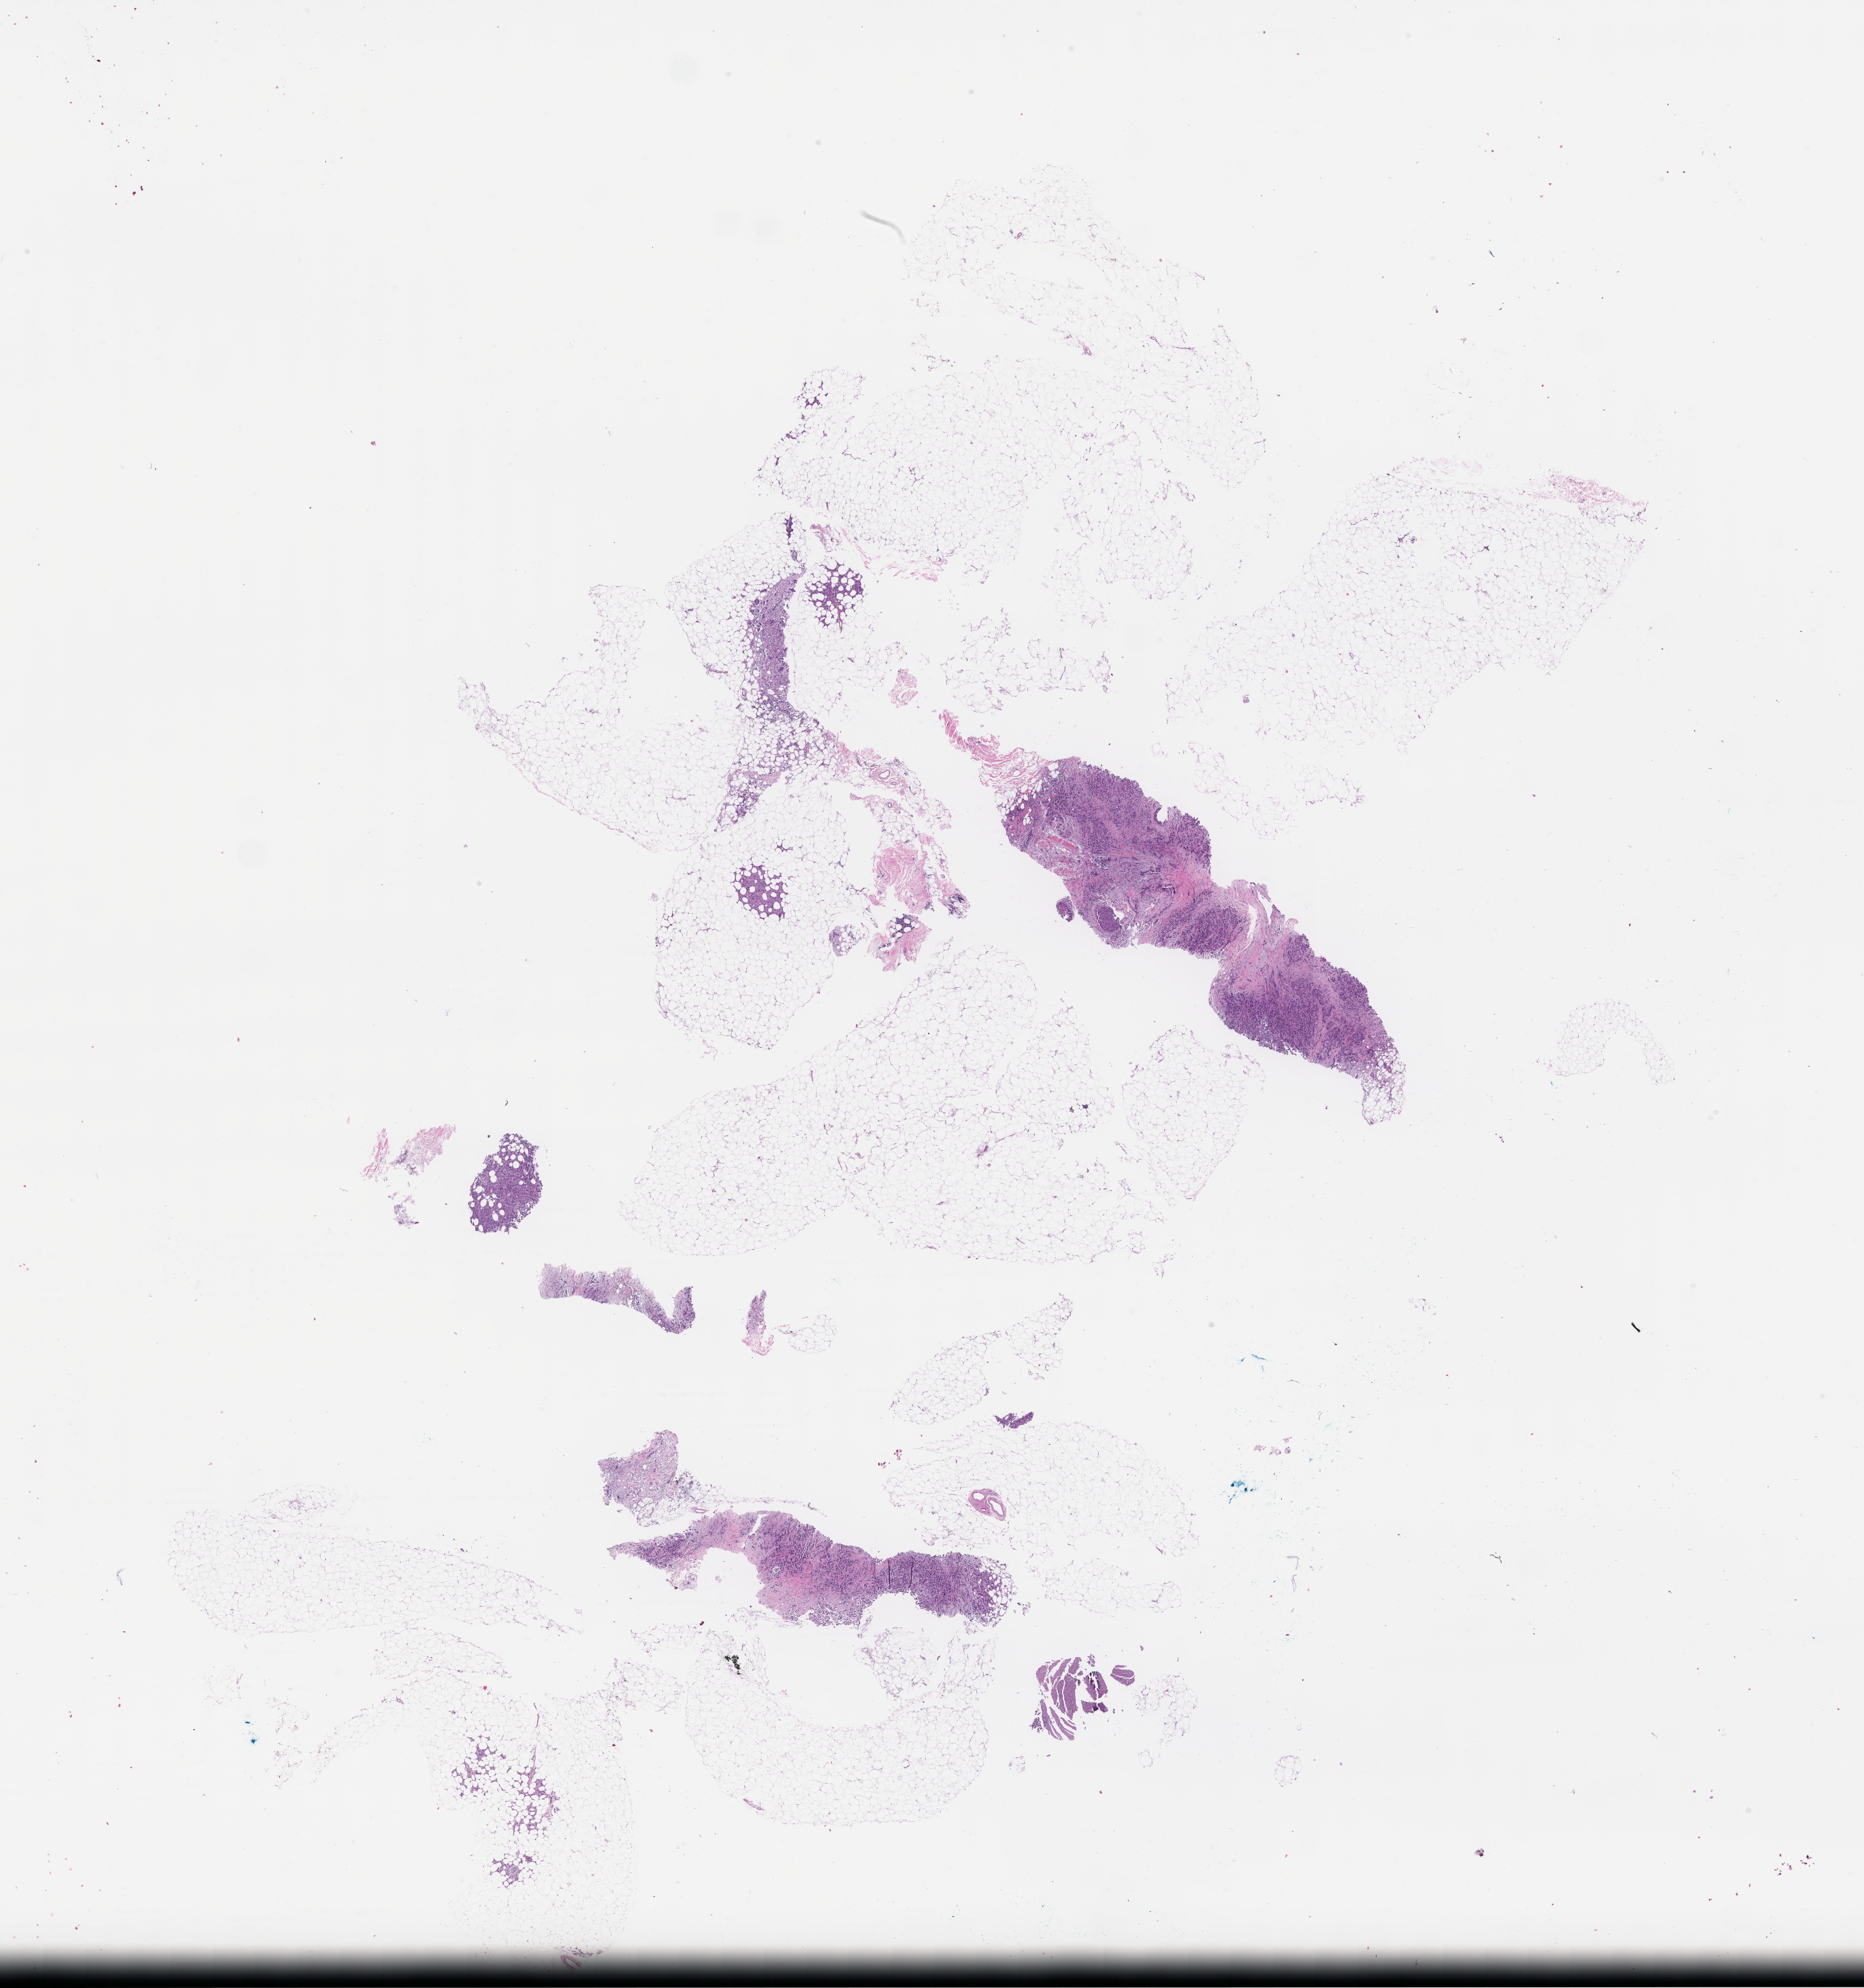
Whole-slide image, hematoxylin and eosin (H&E) stain, whole scanned area (about 22.1 x 23.6 mm) shown as a low-resolution overview, formalin-fixed, paraffin-embedded (FFPE) tissue, tissue site: breast, specimen time point: archival tissue. Patient: female.
* this section: primary tumour tissue
* diagnosis: Invasive Breast Carcinoma